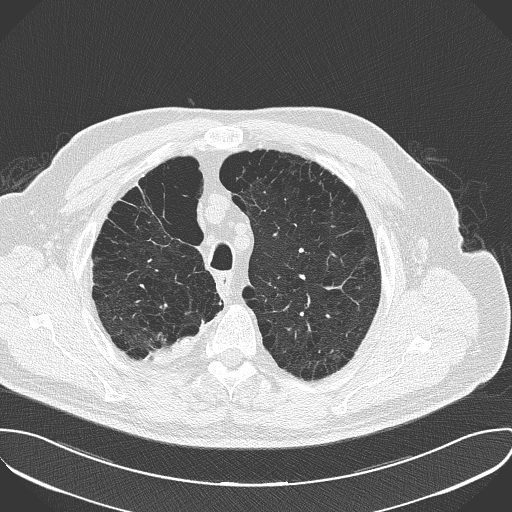
Chest CT (low-dose screening protocol), one axial image, first (baseline) screen, lung window (W 1500 / L -600 HU), 2 mm slice thickness, lung (sharp) reconstruction kernel (B50f), 120 kVp, slice 39 of 181 in the series. Male participant, aged 68 years at enrolment. Current smoker at enrolment.
Expert reader's lesion annotation, box from (x=126, y=324) to (x=196, y=373) px. The screening reader recorded 3 non-calcified nodules or masses ≥4 mm on this exam; which of them this box marks is not recorded. Participant outcome: lung cancer diagnosed 661 days after this screen (after the second annual screen) — adenocarcinoma, NOS, right upper lobe, stage IV (AJCC 6th edition), 29 mm at pathology.